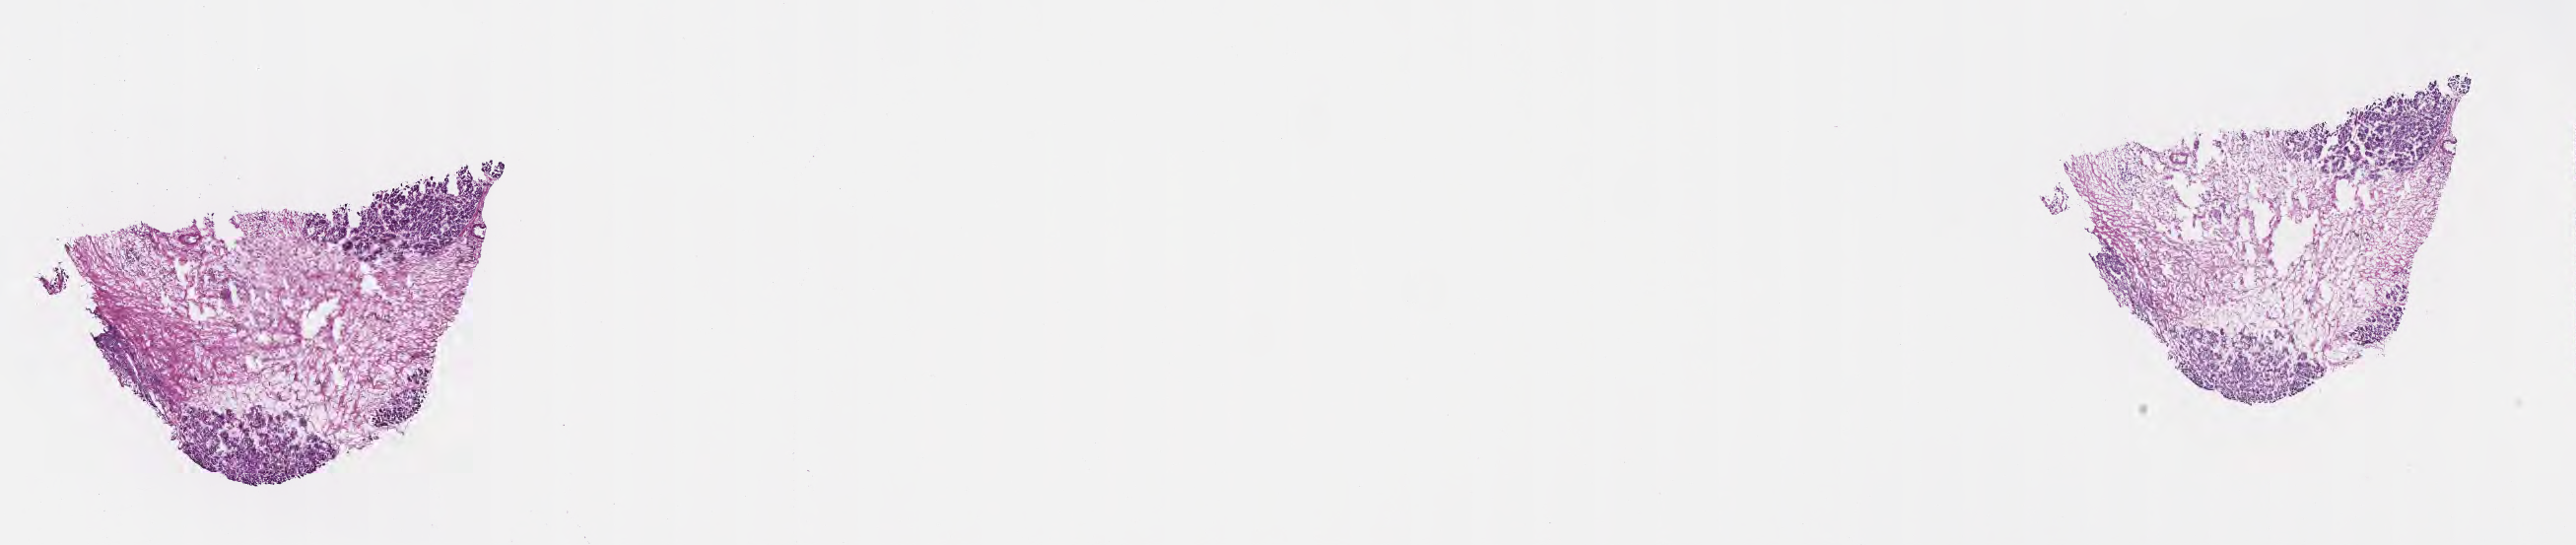
Whole-slide image, hematoxylin and eosin (H&E) stain, a low-resolution overview of the entire scanned area, about 21.1 x 4.5 mm; frozen section (tissue freezing medium); specimen: primary tumor; anatomic site: head of pancreas. Female patient; age at initial diagnosis 71 years. Tumor grade: G3 (poorly differentiated). Composition of this section per pathologist review: tumor cells 22%, tumor nuclei 75%, stromal cells 78%, necrosis 0%, normal cells 0%. Inflammatory infiltration, as recorded: lymphocyte infiltration 20%, monocyte infiltration 1%, neutrophil infiltration 0%.
• AJCC pathologic stage: Stage III
• diagnosis: Infiltrating duct carcinoma, NOS